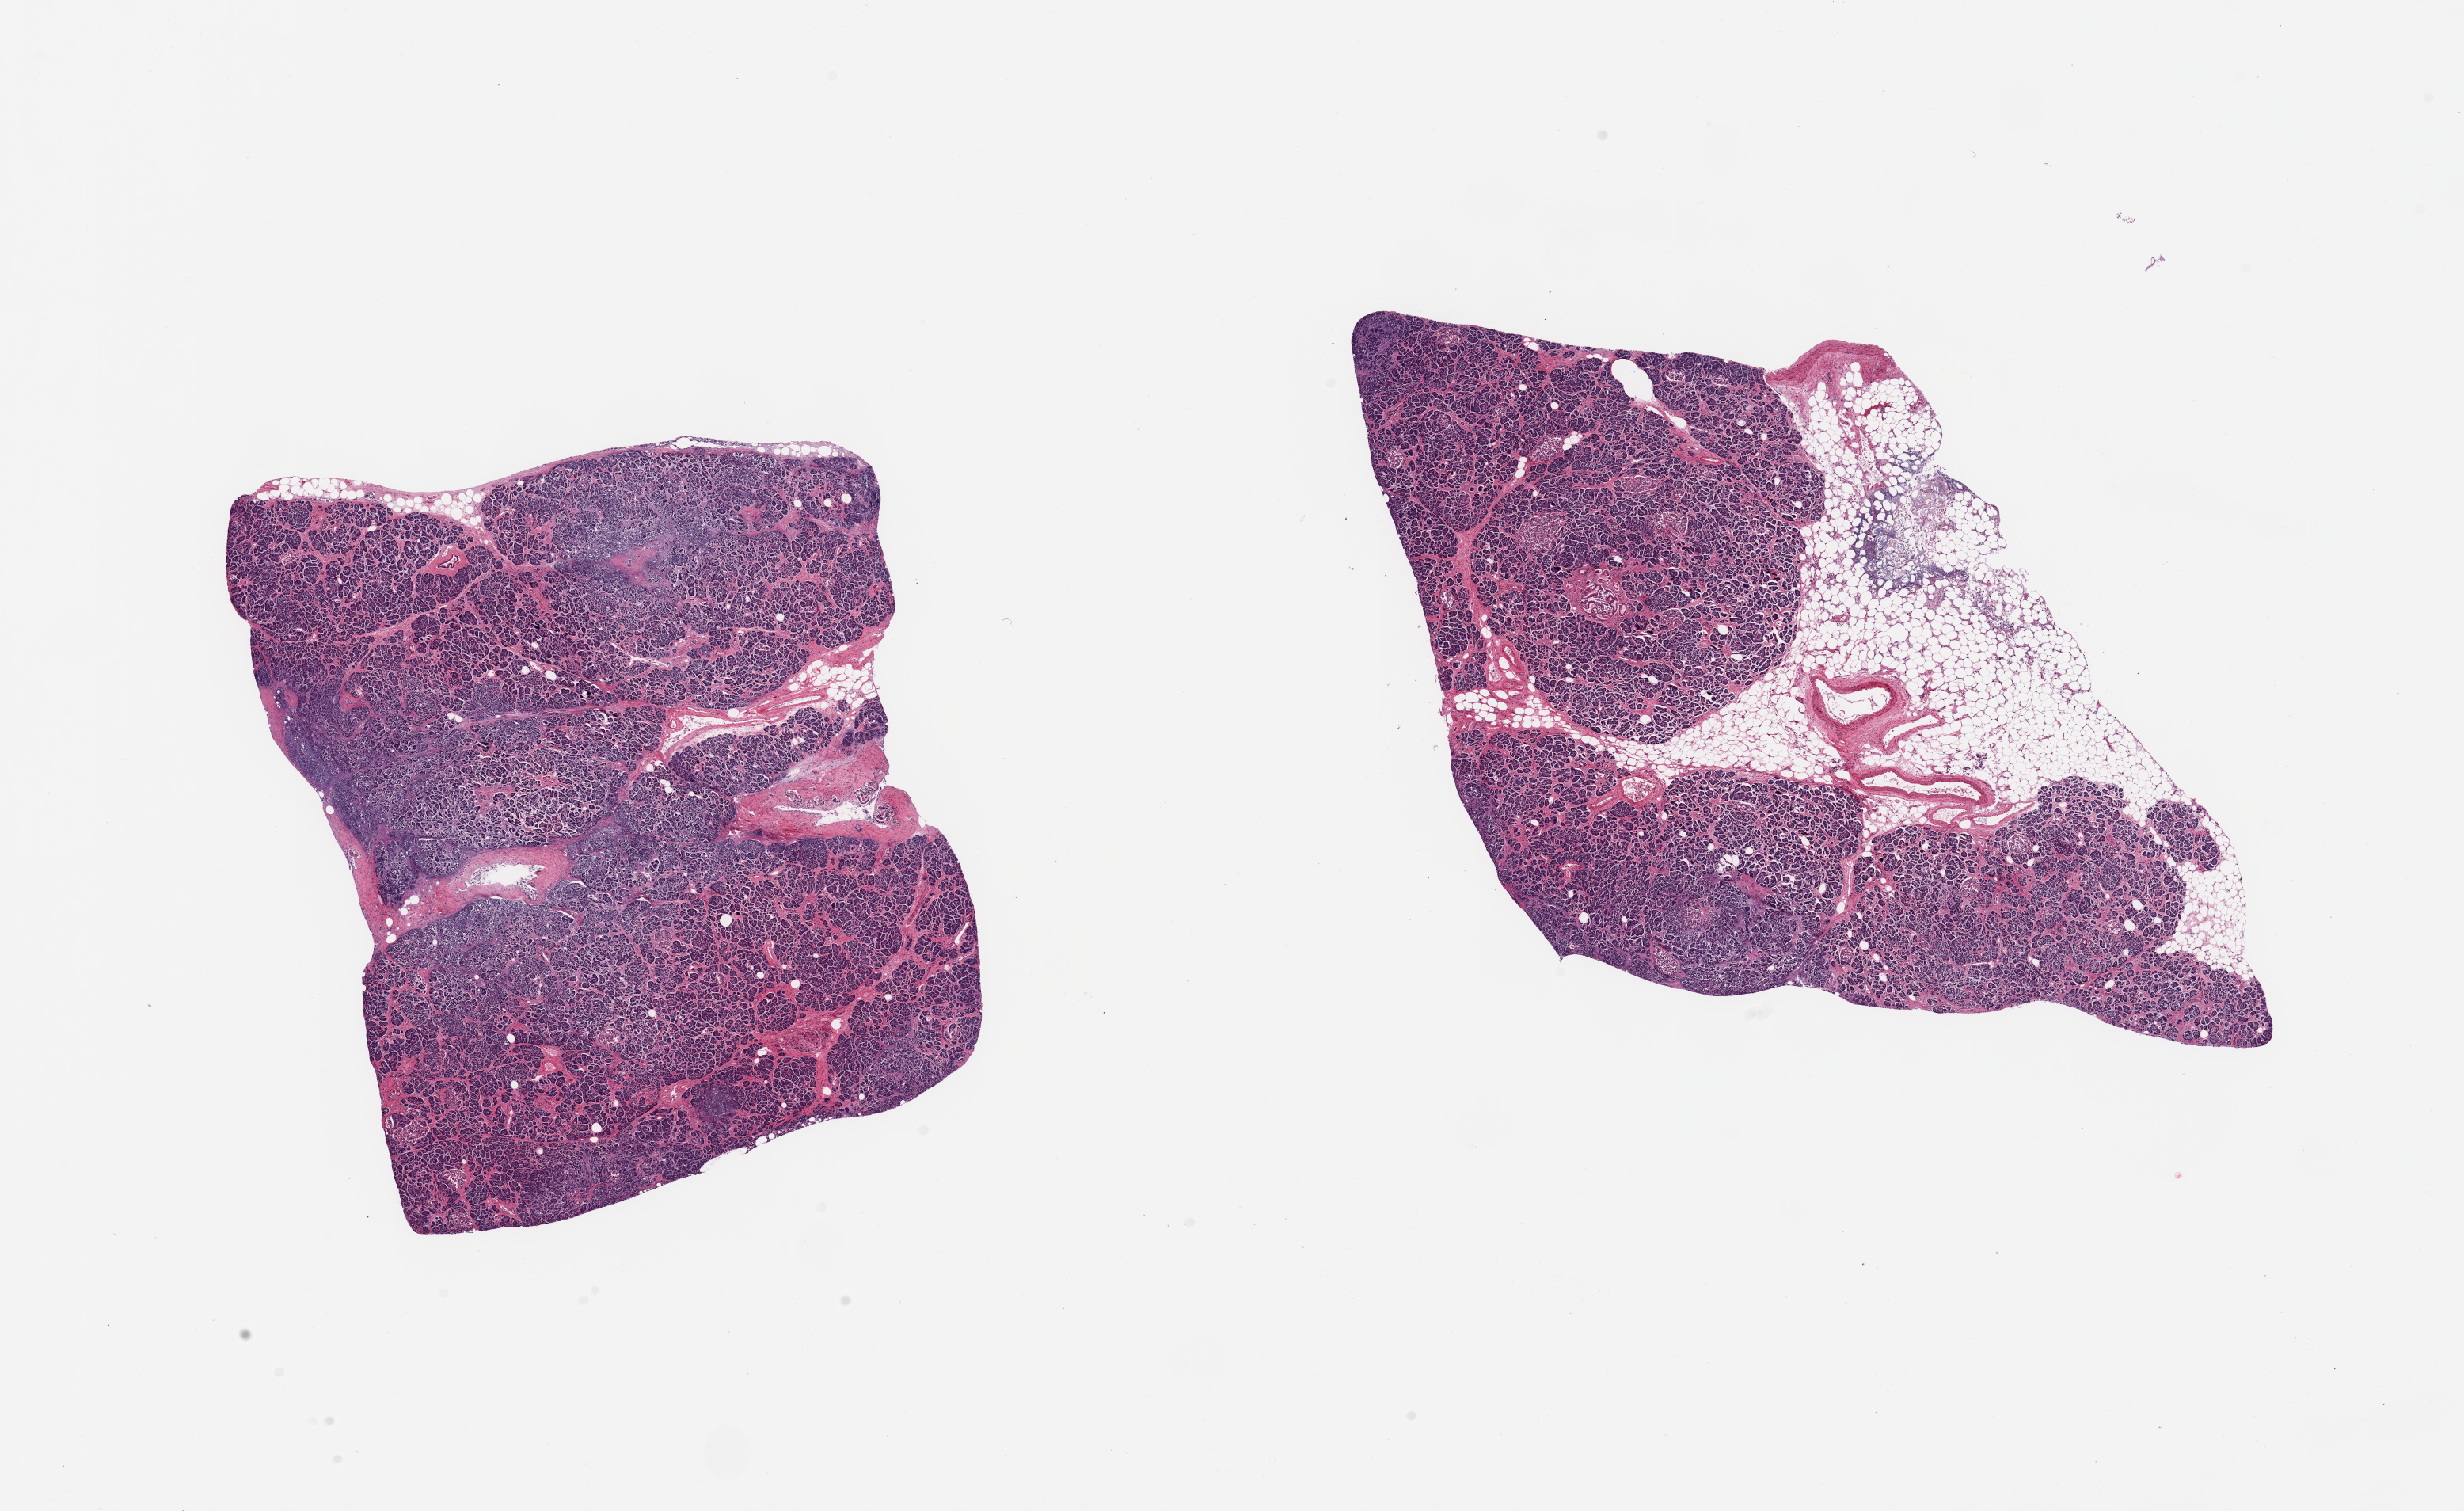
Digitized haematoxylin and eosin-stained section, brightfield — shown as a low-resolution overview of the whole scanned area (about 24.6 x 15.1 mm); PAXgene-fixed, paraffin-embedded tissue; section of pancreas (target tissue); donor tissue sample. Donor sex: male.
Review note (as recorded): 2 pieces, ~25% fat; focal Pan IN (, ungraded due to autolysis); rep Islets, early autolytic changes.